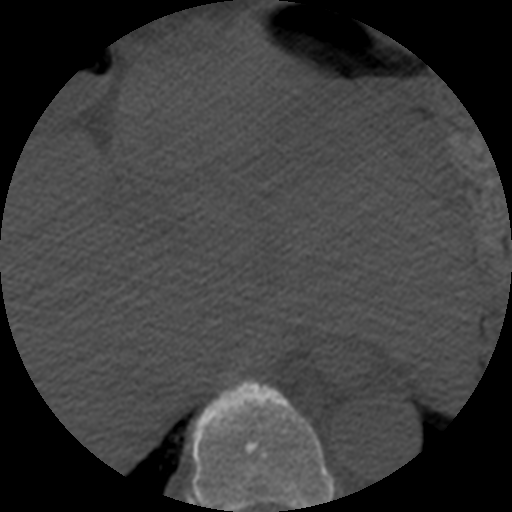
CT including the spine, one axial slice; slice 282 of 508 in the series (ordered by position); 120 kVp; bone window (W 1800 / L 400 HU); 1.25 mm slice thickness; 512 × 512 image matrix, field of view 160 × 160 mm. Patient age 57 years. From the clinical record (not read from this slice): primary cancer: prostate.
Structures marked on this image (semi-automatically segmented with operator editing):
- T9 vertebra: bounding box <186,380,335,512> (left, top, right, bottom; pixels)